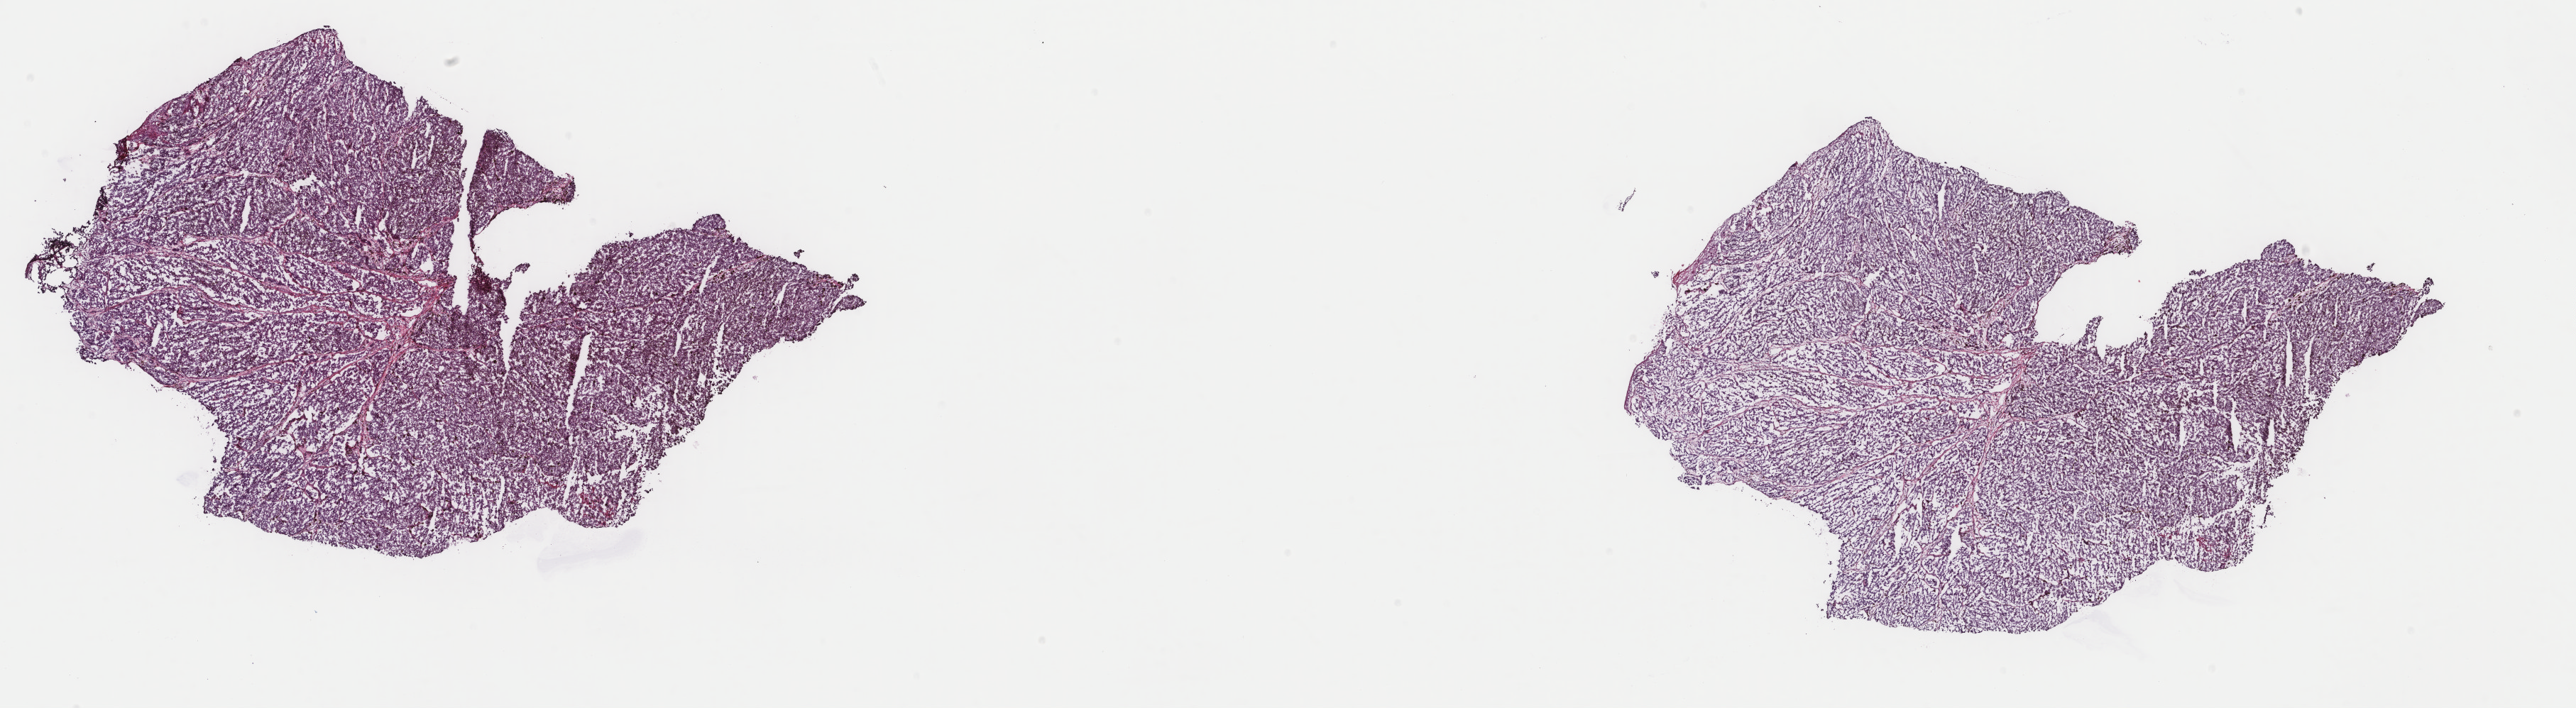
Whole-slide histology image, H&E-stained — a low-resolution overview of the entire scanned area, about 28.8 x 7.9 mm. Frozen section. Primary tumour sample from the skin. Patient: male, age at initial diagnosis 63 years. Pathologist review of this section (percent, as recorded): tumour cells 100%, tumour nuclei 96%.
Pathologic diagnosis: Malignant melanoma, NOS.